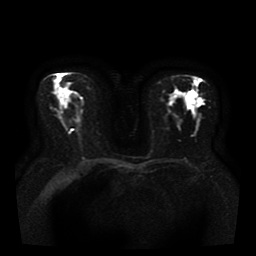
Breast MRI, one axial slice. Slice 18 of 36 in the series (ordered by position). Diffusion-weighted series; image 2 of 4 stored at this slice position (different b-values; order by instance number). 1.5 T. 256 × 256 image matrix, field of view 330 × 330 mm. Female patient.
Structures marked on this image (expert manual segmentation):
- tumour on diffusion-weighted imaging: box from (x=190, y=94) to (x=201, y=108) px